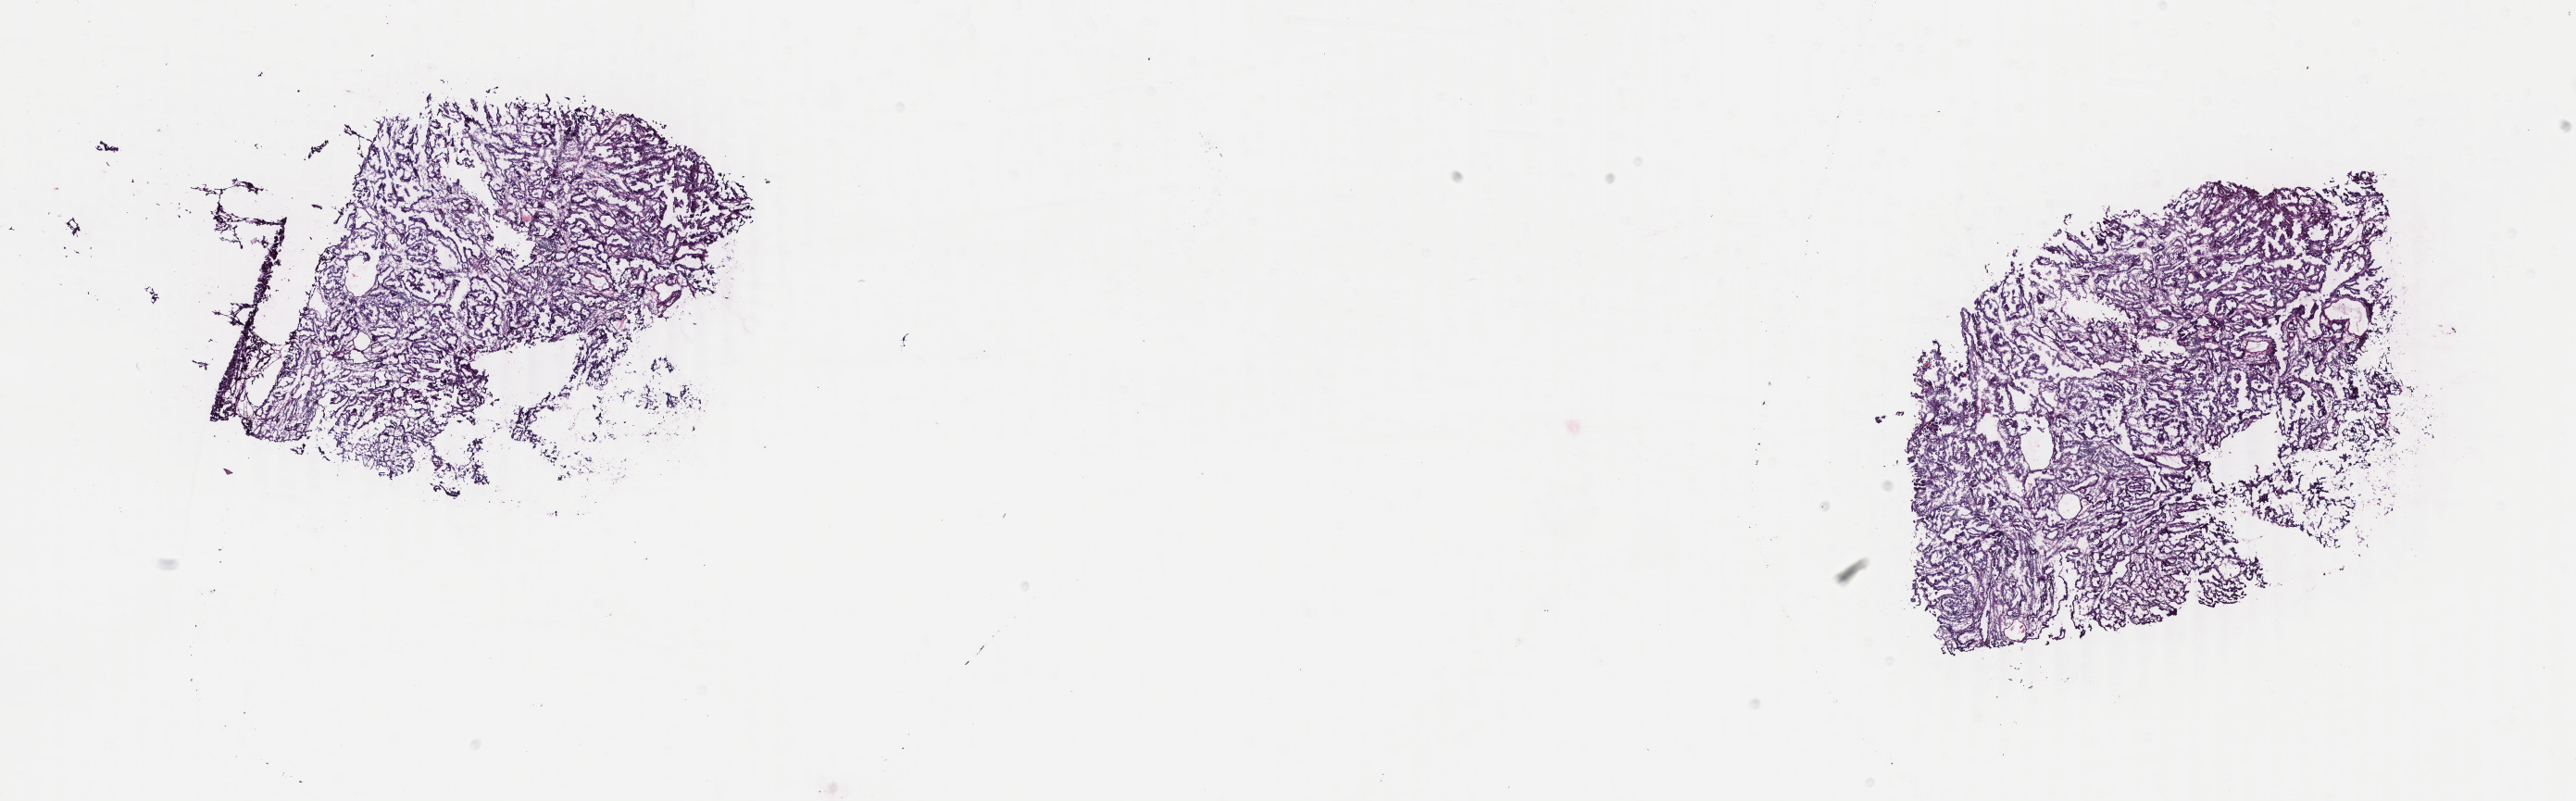
Digitized H&E tissue section (whole slide) — low-resolution overview of the scanned area, about 22.1 x 6.9 mm (acquisition: 40x scan), frozen section, sample: primary tumour, uterus. Female, age 71 years at initial diagnosis.
Histologic diagnosis: Serous cystadenocarcinoma, NOS.